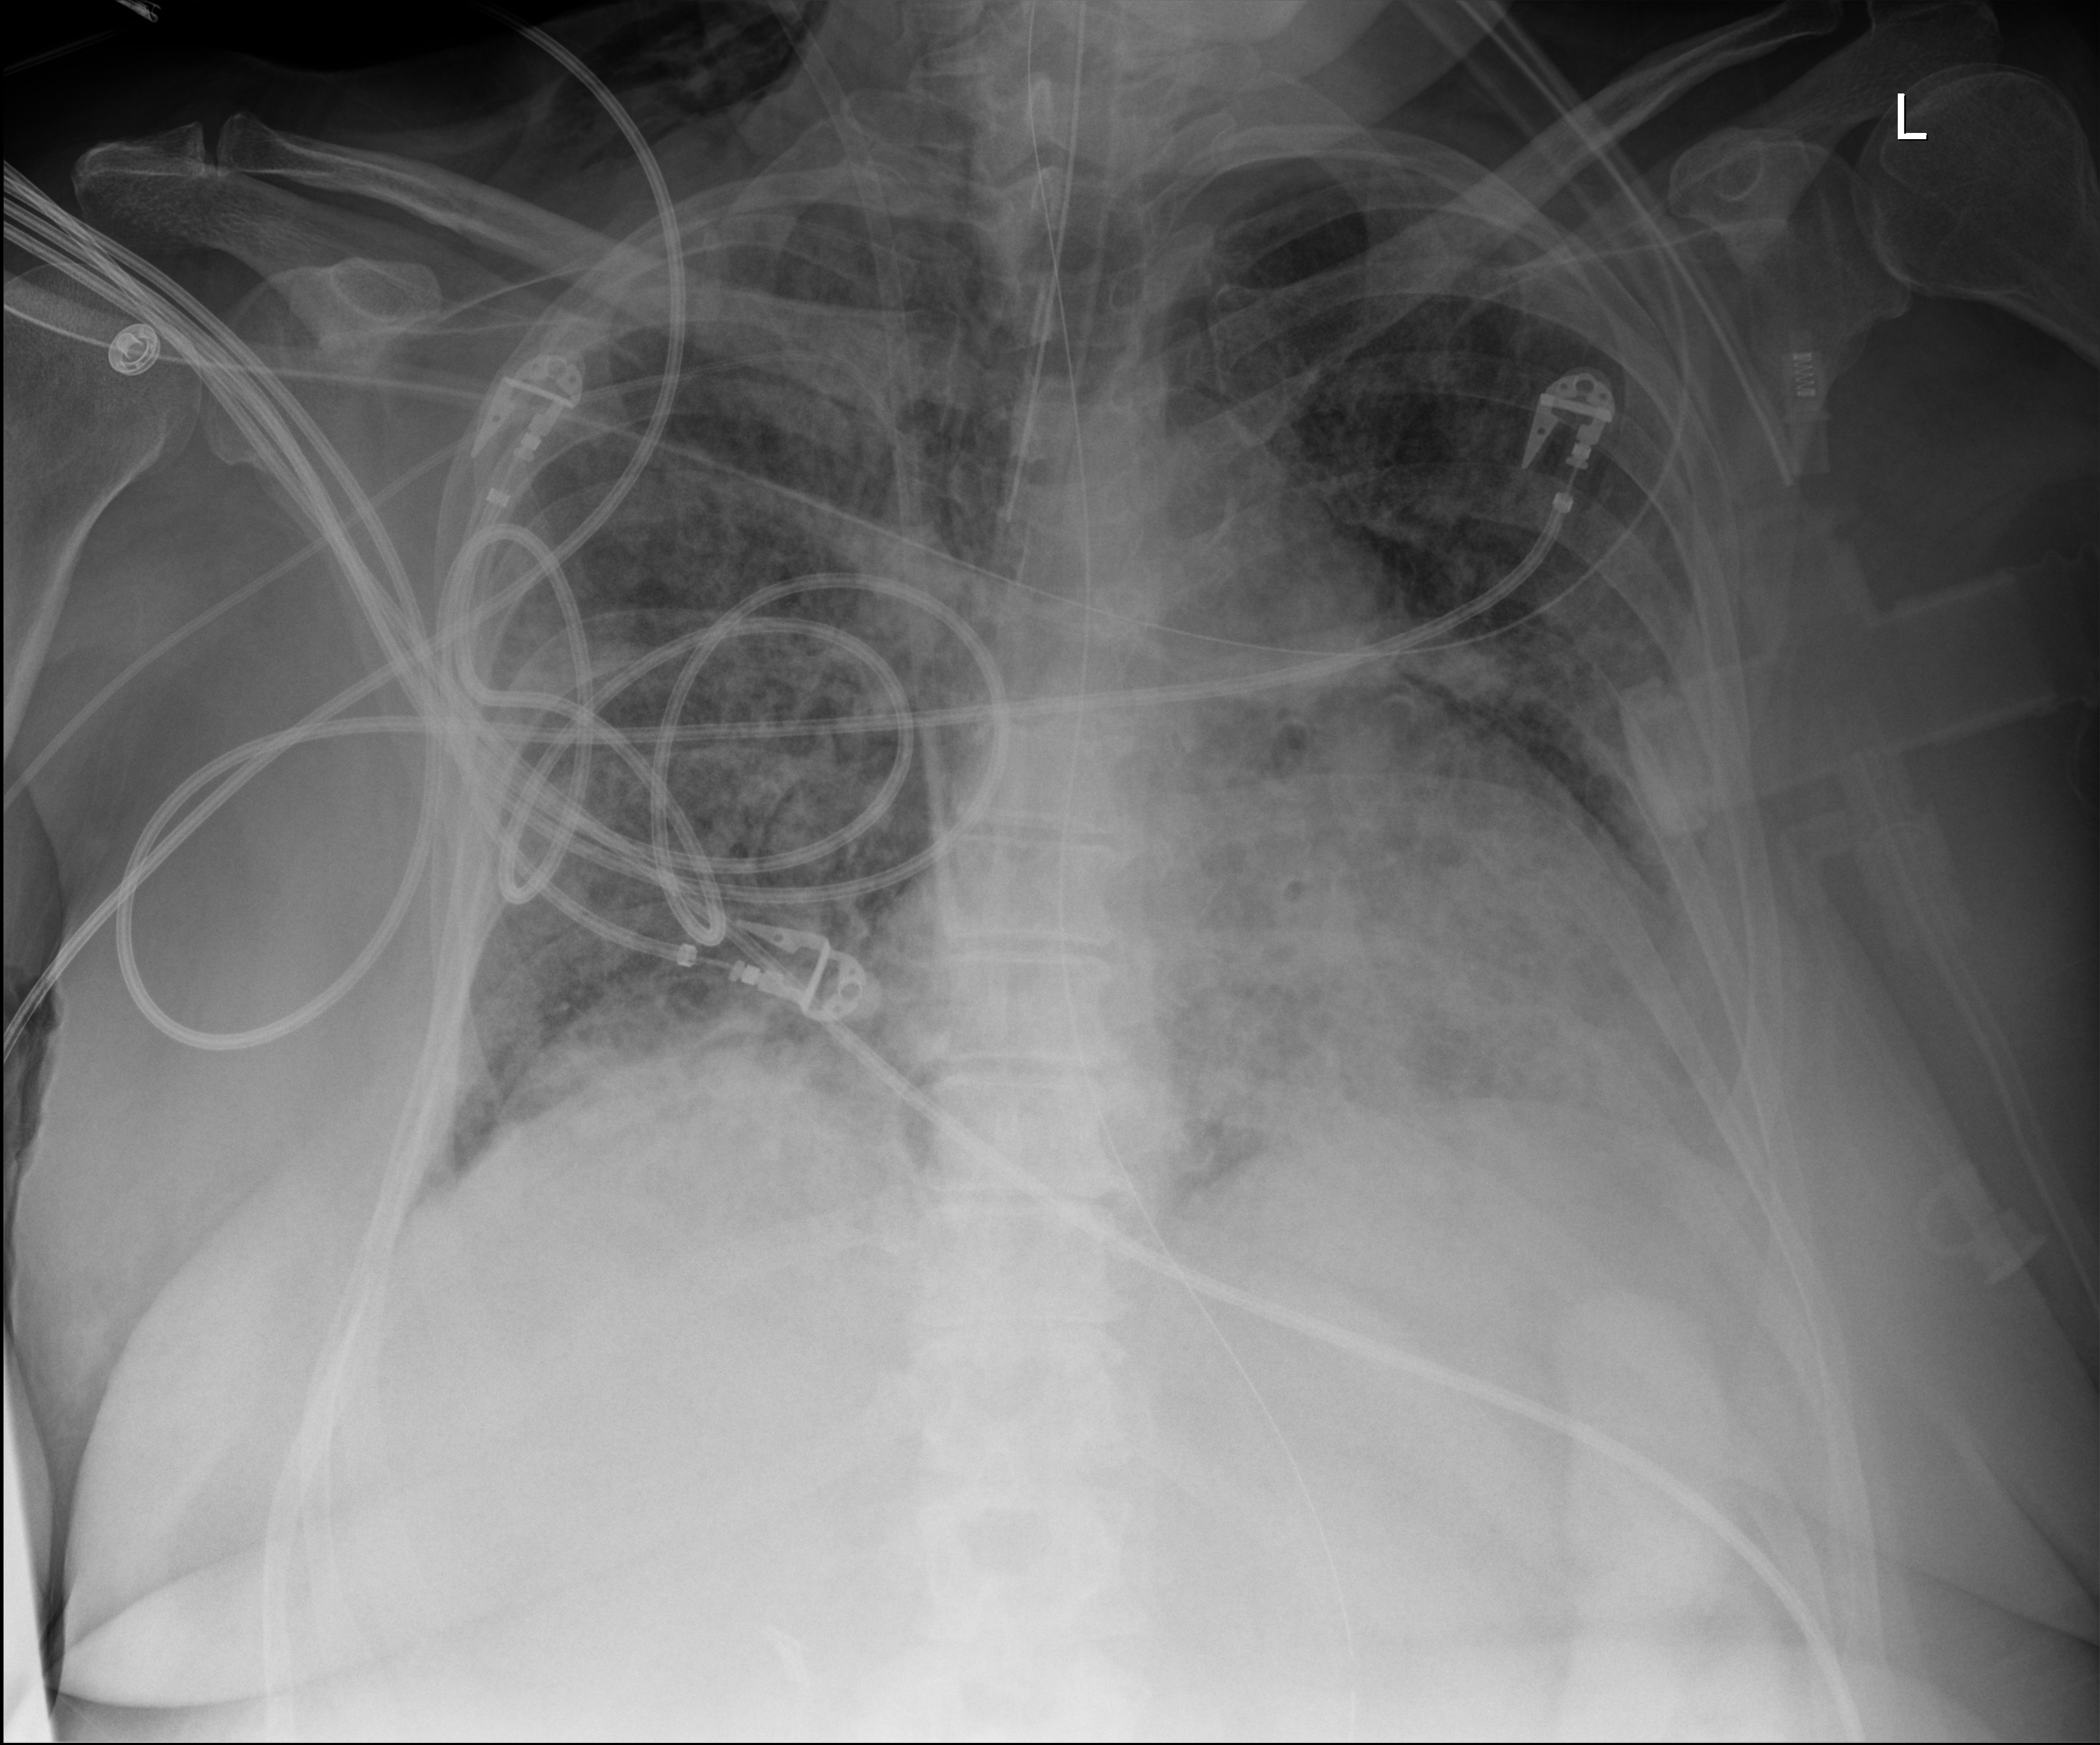
Chest X-ray, anteroposterior (AP) projection. Female patient hospitalised with COVID-19, age 60–74 years.
From the hospital-stay record, not from the radiograph (when in the stay this image was taken is not recorded): mechanically ventilated during this hospital stay: yes; diabetes (admission record): no; admitted to intensive care during this hospital stay: yes.